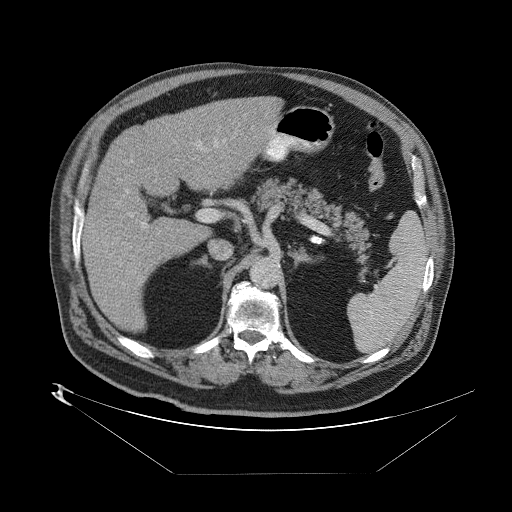
Contrast-enhanced abdominal CT (liver protocol), one axial slice. Position 42 of 89 along the scan axis. 140 kVp. One of 2 acquisitions stored at this slice position. Soft-tissue window (W 400 / L 40 HU). 2.5 mm slice thickness. 512 × 512 image matrix. From the clinical record (not read from this slice): diagnosis: hepatocellular carcinoma (patient treated with transarterial chemoembolisation; whether this scan precedes or follows treatment is not stated here); TNM stage (as recorded): Stage-II; Child-Pugh class: B; tumour differentiation: moderately differentiated; tumour nodularity: multinodular.
Structures marked on this image (semi-automatic segmentation, software-assisted and operator-edited):
- abdominal aorta: bounding box <251,259,278,287> (left, top, right, bottom; pixels)
- liver parenchyma outside the tumour (the mass and vessels are separate outlines, so this box may not span the whole liver): <82,94,280,334>
- liver vessels: <90,138,202,286>